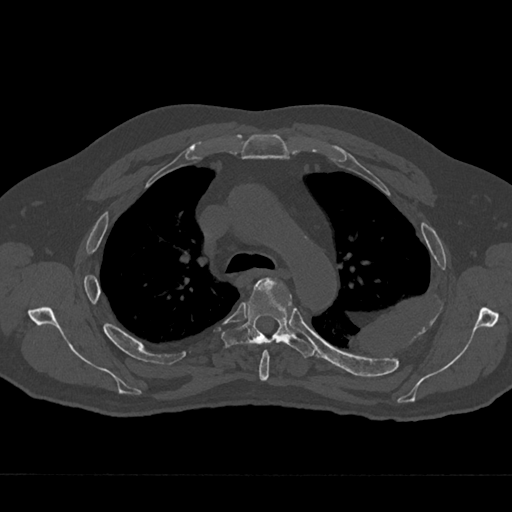
CT including the spine, one axial slice; slice 489 of 797 in the series (ordered by position); 120 kVp; bone window (W 1800 / L 400 HU); 0.5 mm slice thickness; 512 × 512 image matrix, field of view 377 × 377 mm. Male patient, age 75 years. From the clinical record (not read from this slice): primary cancer: renal.
Annotated regions visible in this slice (semi-automatic segmentation, software-assisted and operator-edited):
- T4 vertebra: bounding box <259,350,270,381> (left, top, right, bottom; pixels)
- T5 vertebra: <221,277,316,358>